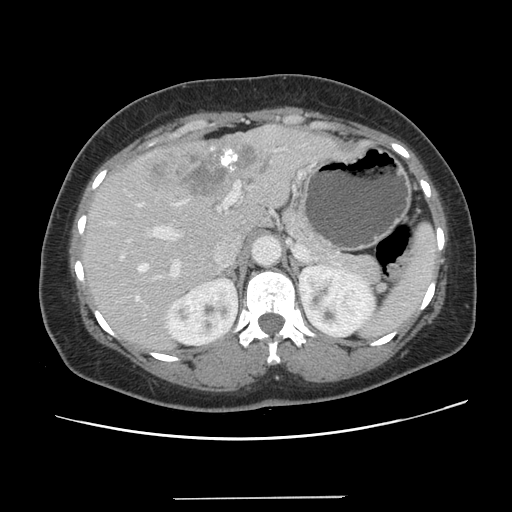
Contrast-enhanced abdominal CT, one axial slice; position 86 of 141 along the scan axis; intravenous contrast given; soft-tissue window (W 400 / L 40 HU); 2.5 mm slice thickness; 512 × 512 image matrix, field of view 366 × 366 mm. Female patient, age 53 years. Case-level facts recorded for this patient, not image findings: diagnosis: colorectal cancer liver metastases, imaged before liver resection.
Structures marked on this image (outlined manually by an expert reader):
- hepatic veins: box from (x=136, y=202) to (x=181, y=300) px
- liver: (x=82, y=126)–(x=365, y=351)
- planned liver remnant (the part of the liver to remain after resection): (x=84, y=207)–(x=264, y=351)
- portal vein (with intrahepatic branches): (x=120, y=181)–(x=239, y=281)
- liver metastasis: (x=144, y=141)–(x=271, y=196)